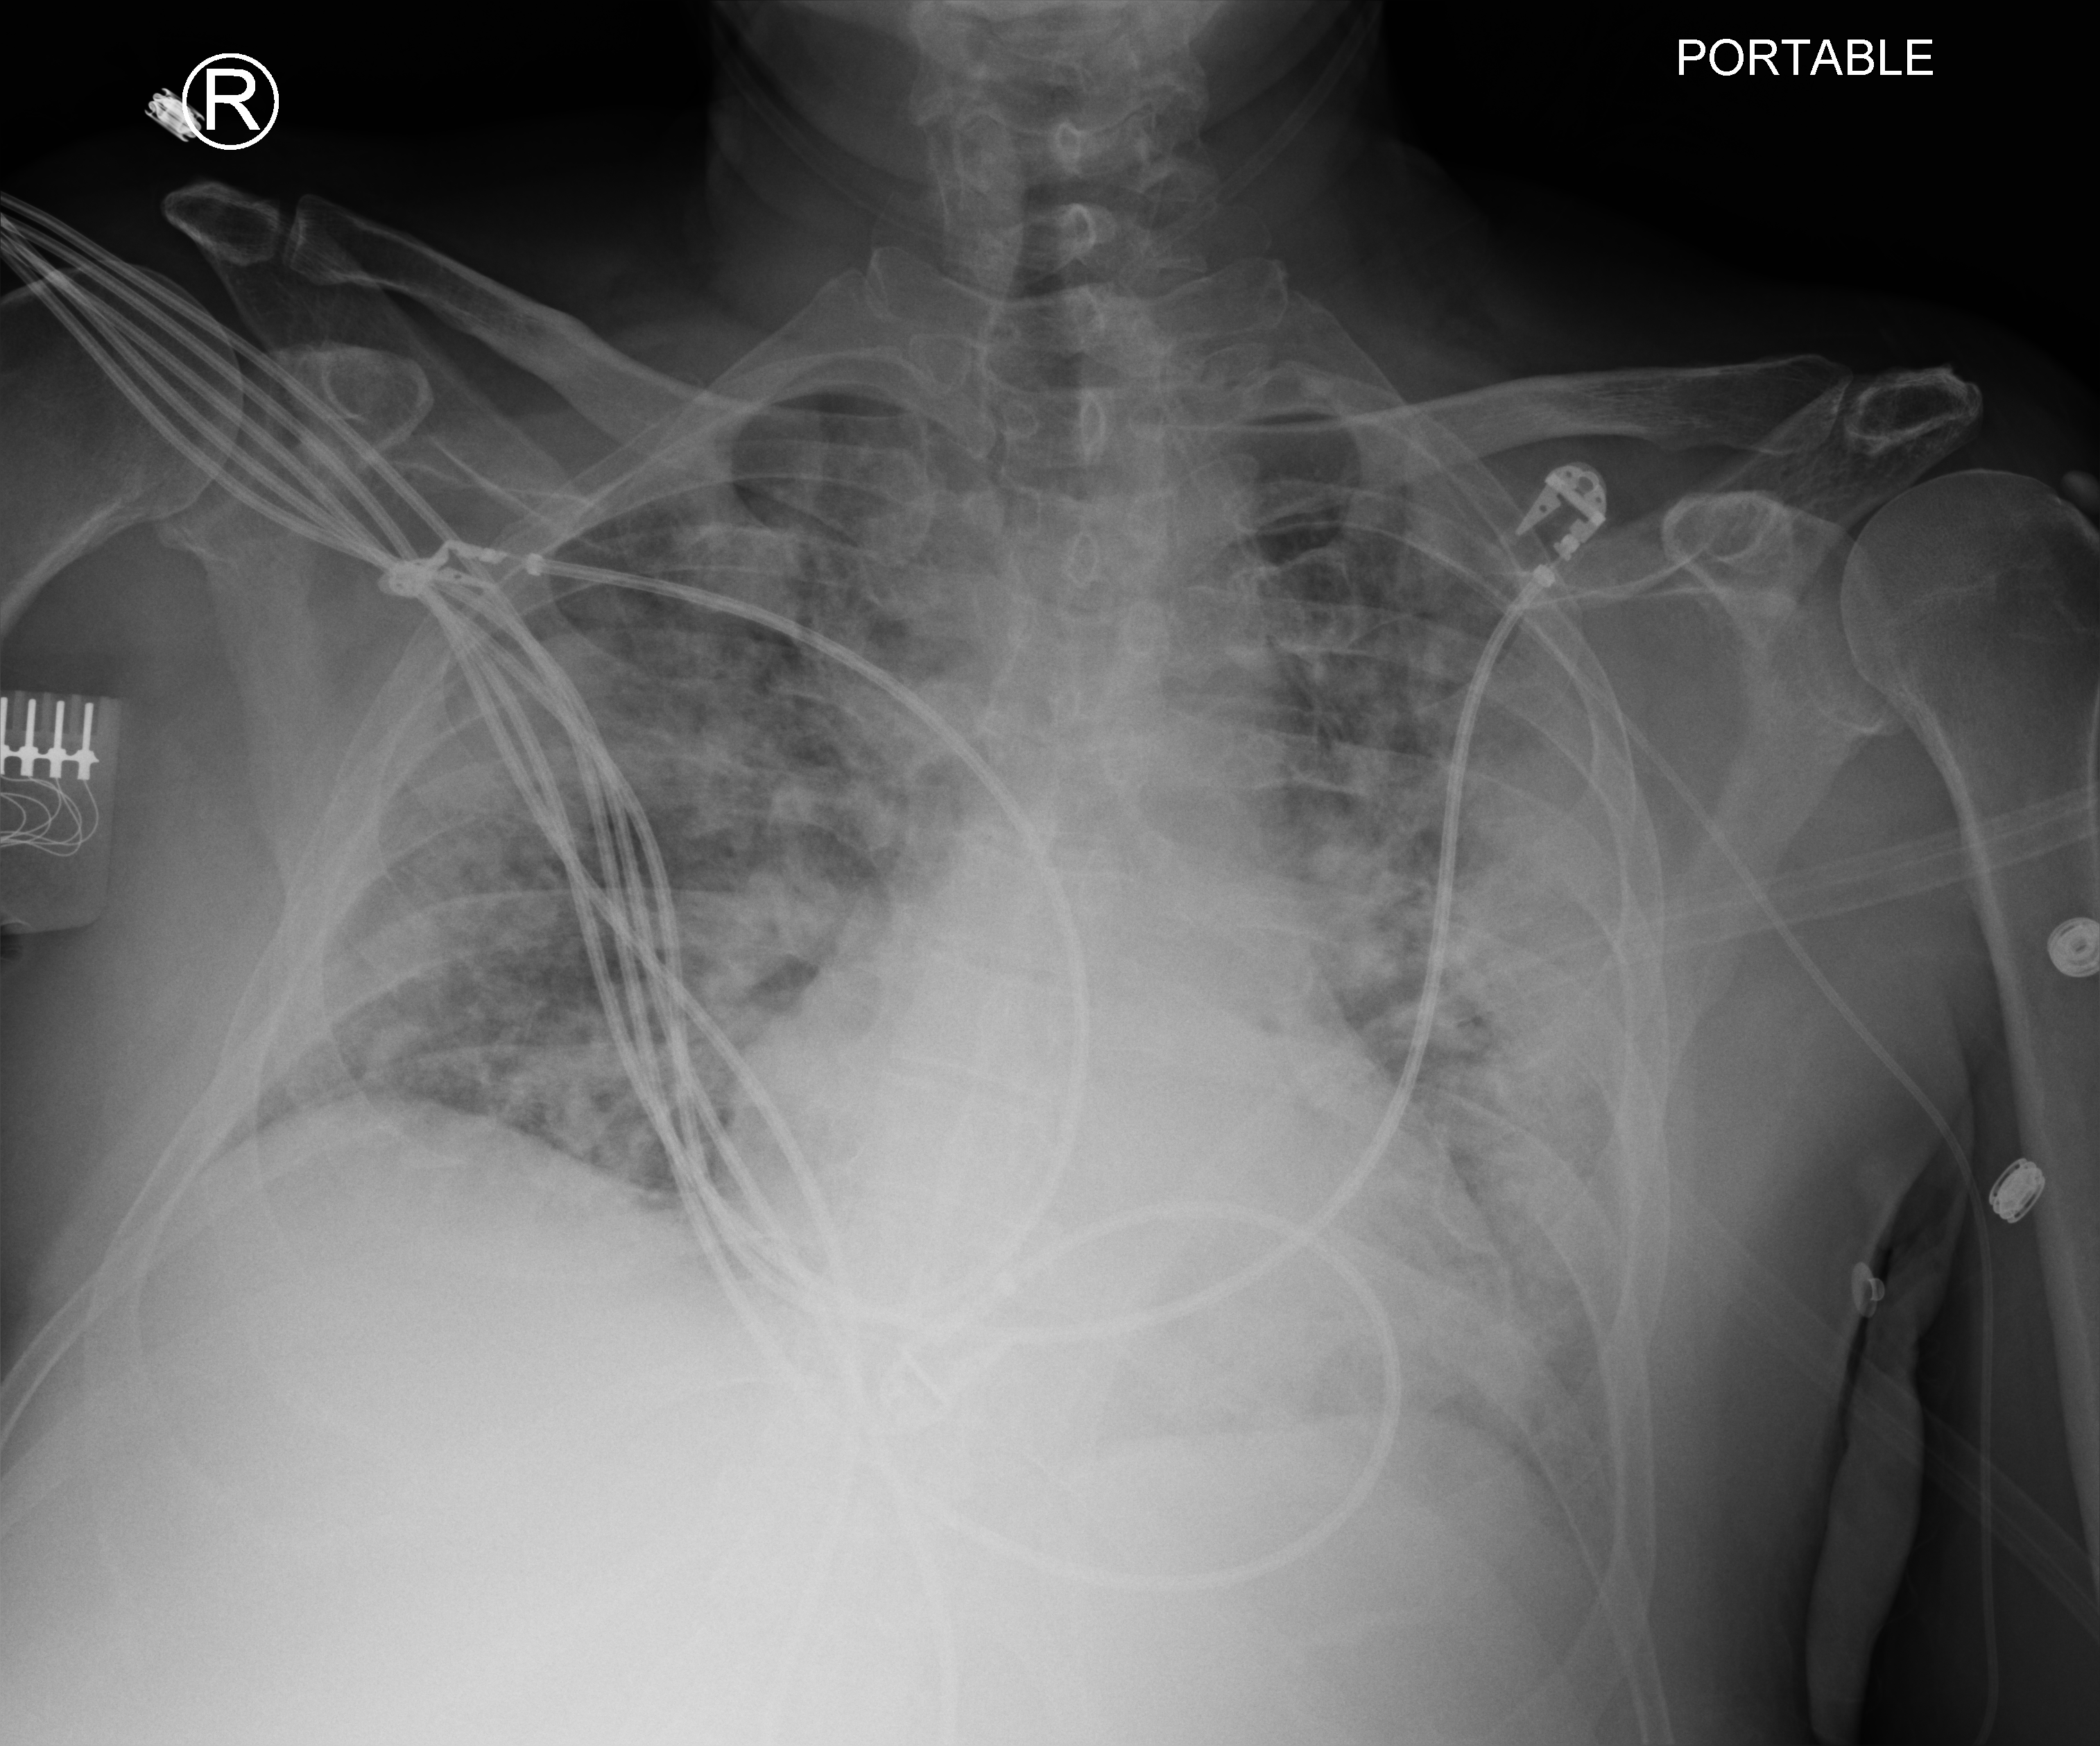
Portable chest radiograph; anteroposterior (AP) projection. Male patient hospitalised with COVID-19, age 18–59 years.
From the hospital-stay record, not from the radiograph (when in the stay this image was taken is not recorded): length of hospital stay: 25 days; smoking status (admission record): never.